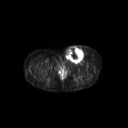
FDG PET of an extremity soft-tissue mass (from a PET/CT study), one axial slice. Position 57 of 267 along the scan axis. 128 × 128 image matrix. Patient: female, 24 years. From the clinical record (not read from this slice): histological type: leiomyosarcoma; grade: high; site of the primary tumour: groin.
Outlined on this slice (expert contour drawn on MRI and transferred to this co-registered scan by the dataset authors):
- gross tumour volume including surrounding oedema: bounding box <64,44,88,63> (left, top, right, bottom; pixels)
- gross tumour volume (mass): <65,46,84,62>